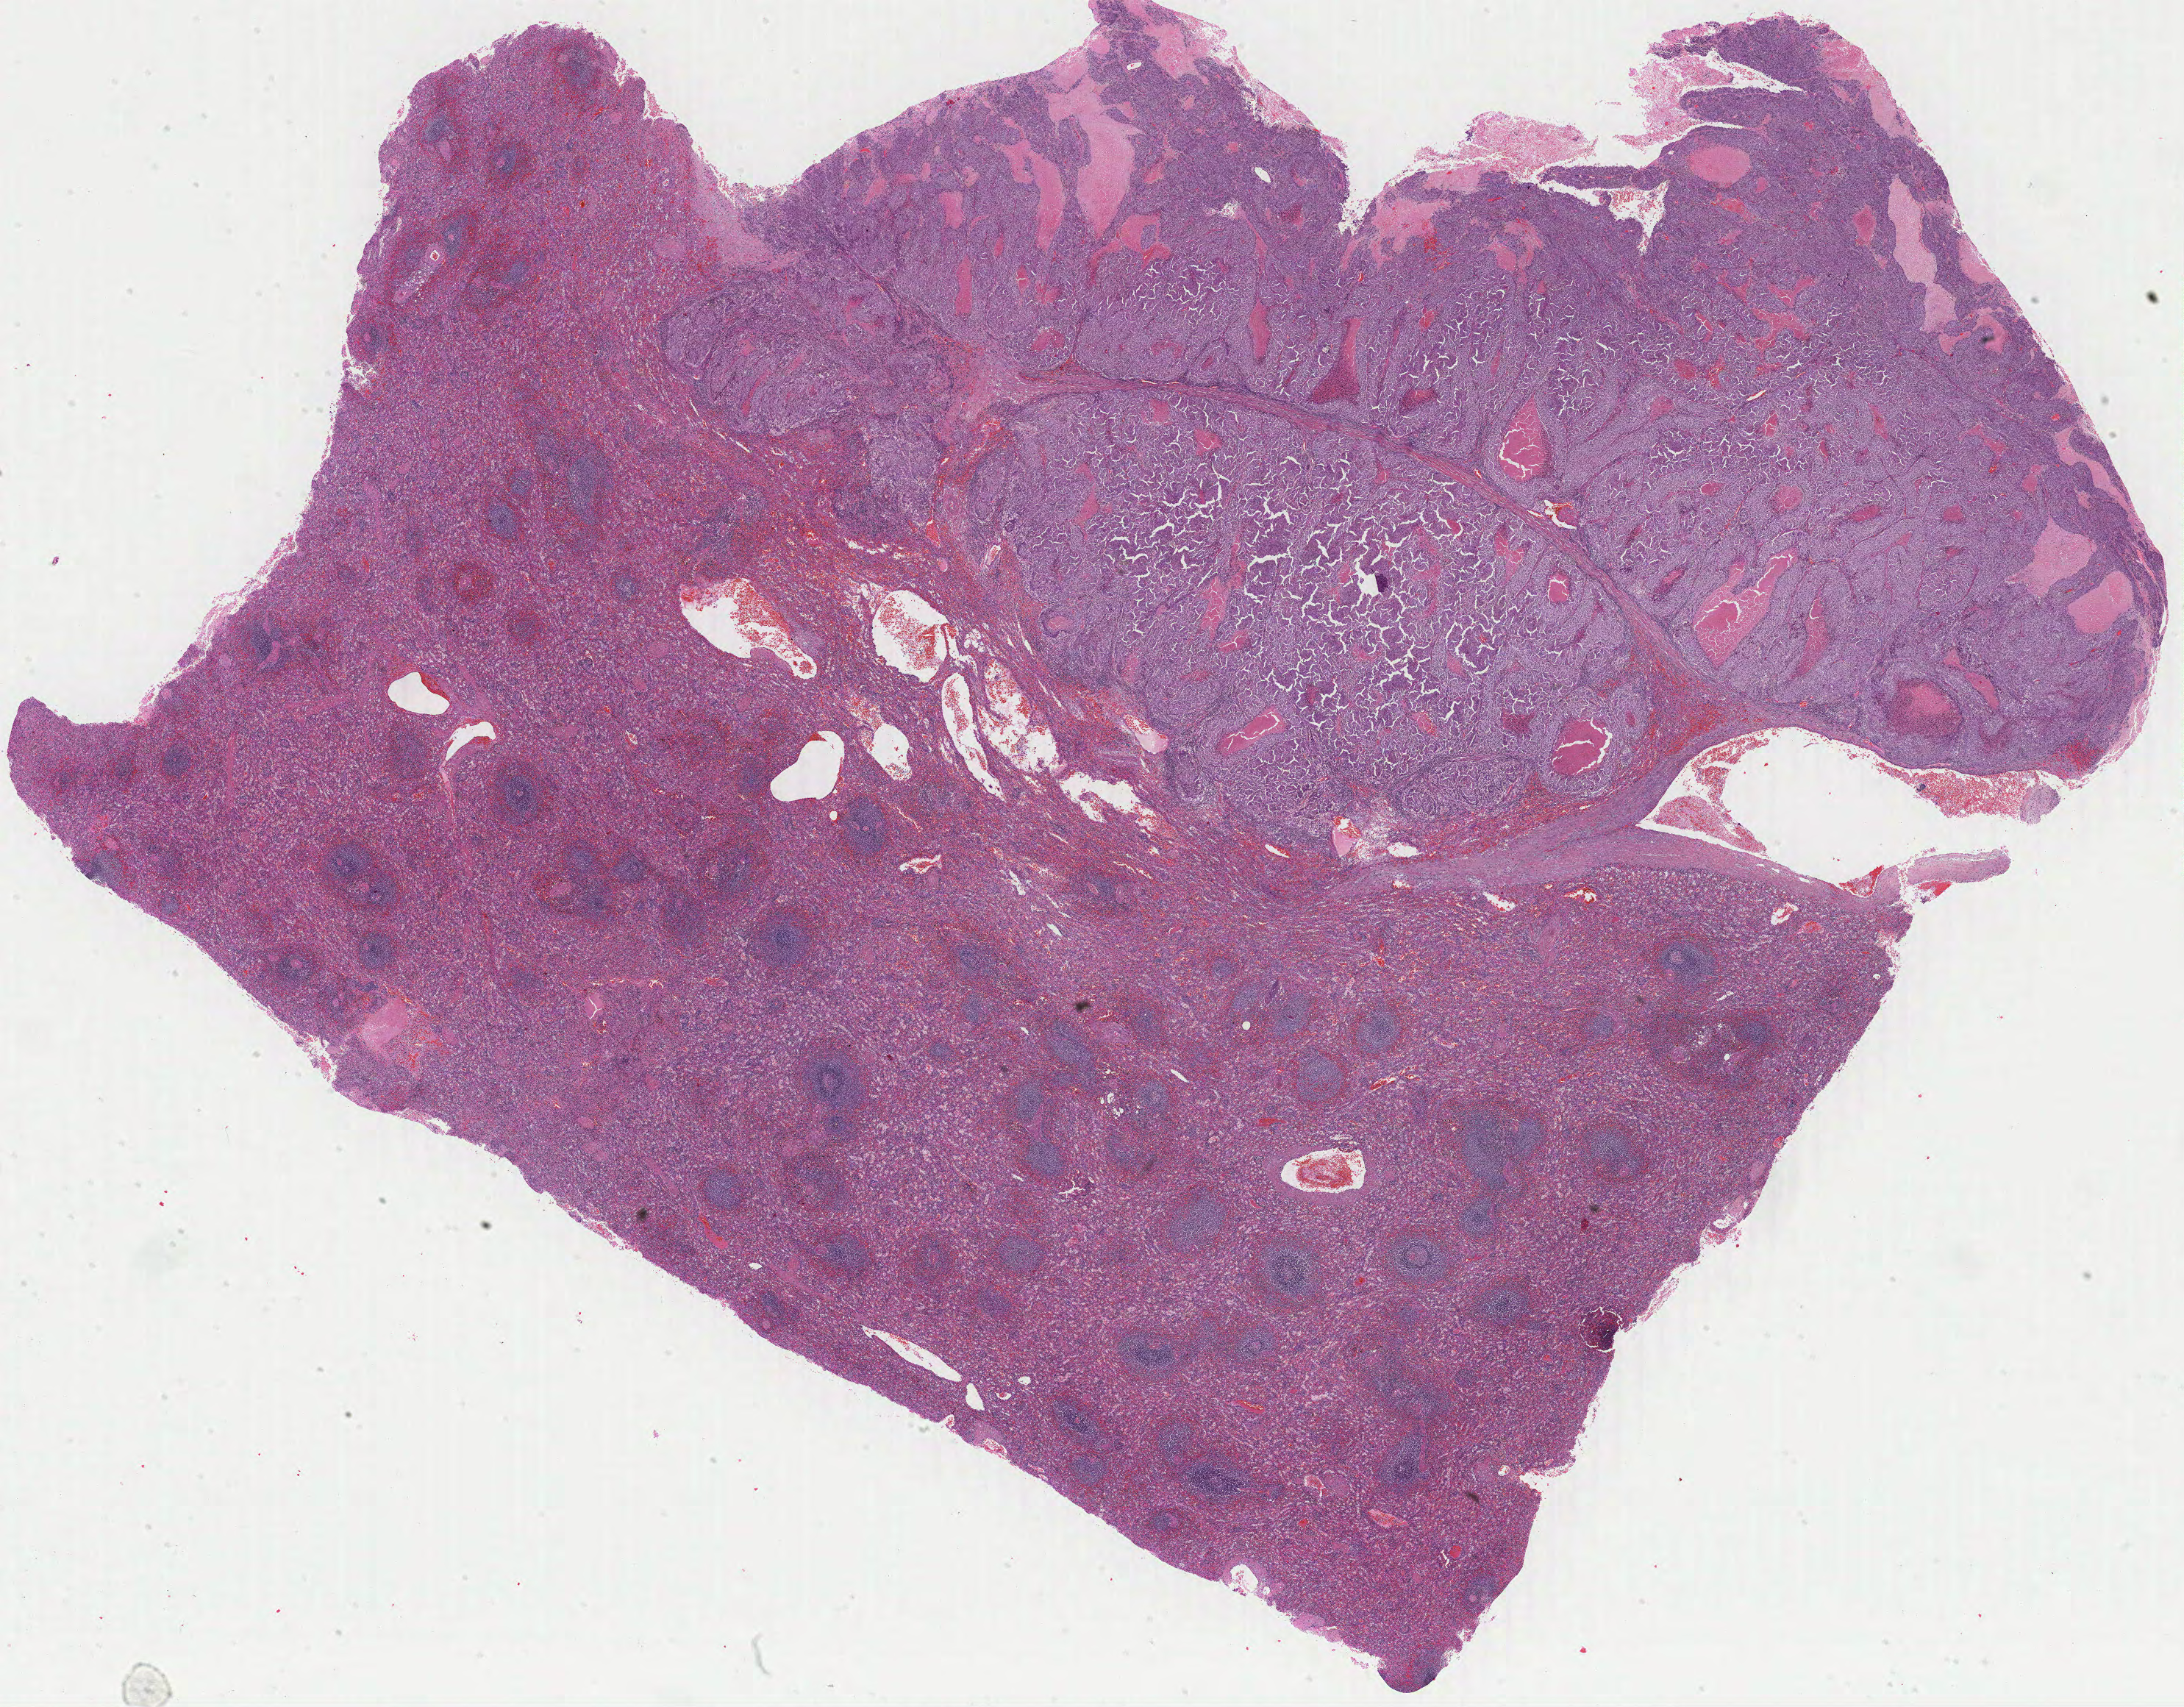
H&E whole-slide image — whole scanned area (about 23.8 x 18.6 mm) shown as a low-resolution overview. FFPE section. Additional metastatic tumour sample. Patient: male, age at initial diagnosis 55 years.
- this section: metastatic tumour tissue
- patient diagnosis: Malignant melanoma, NOS